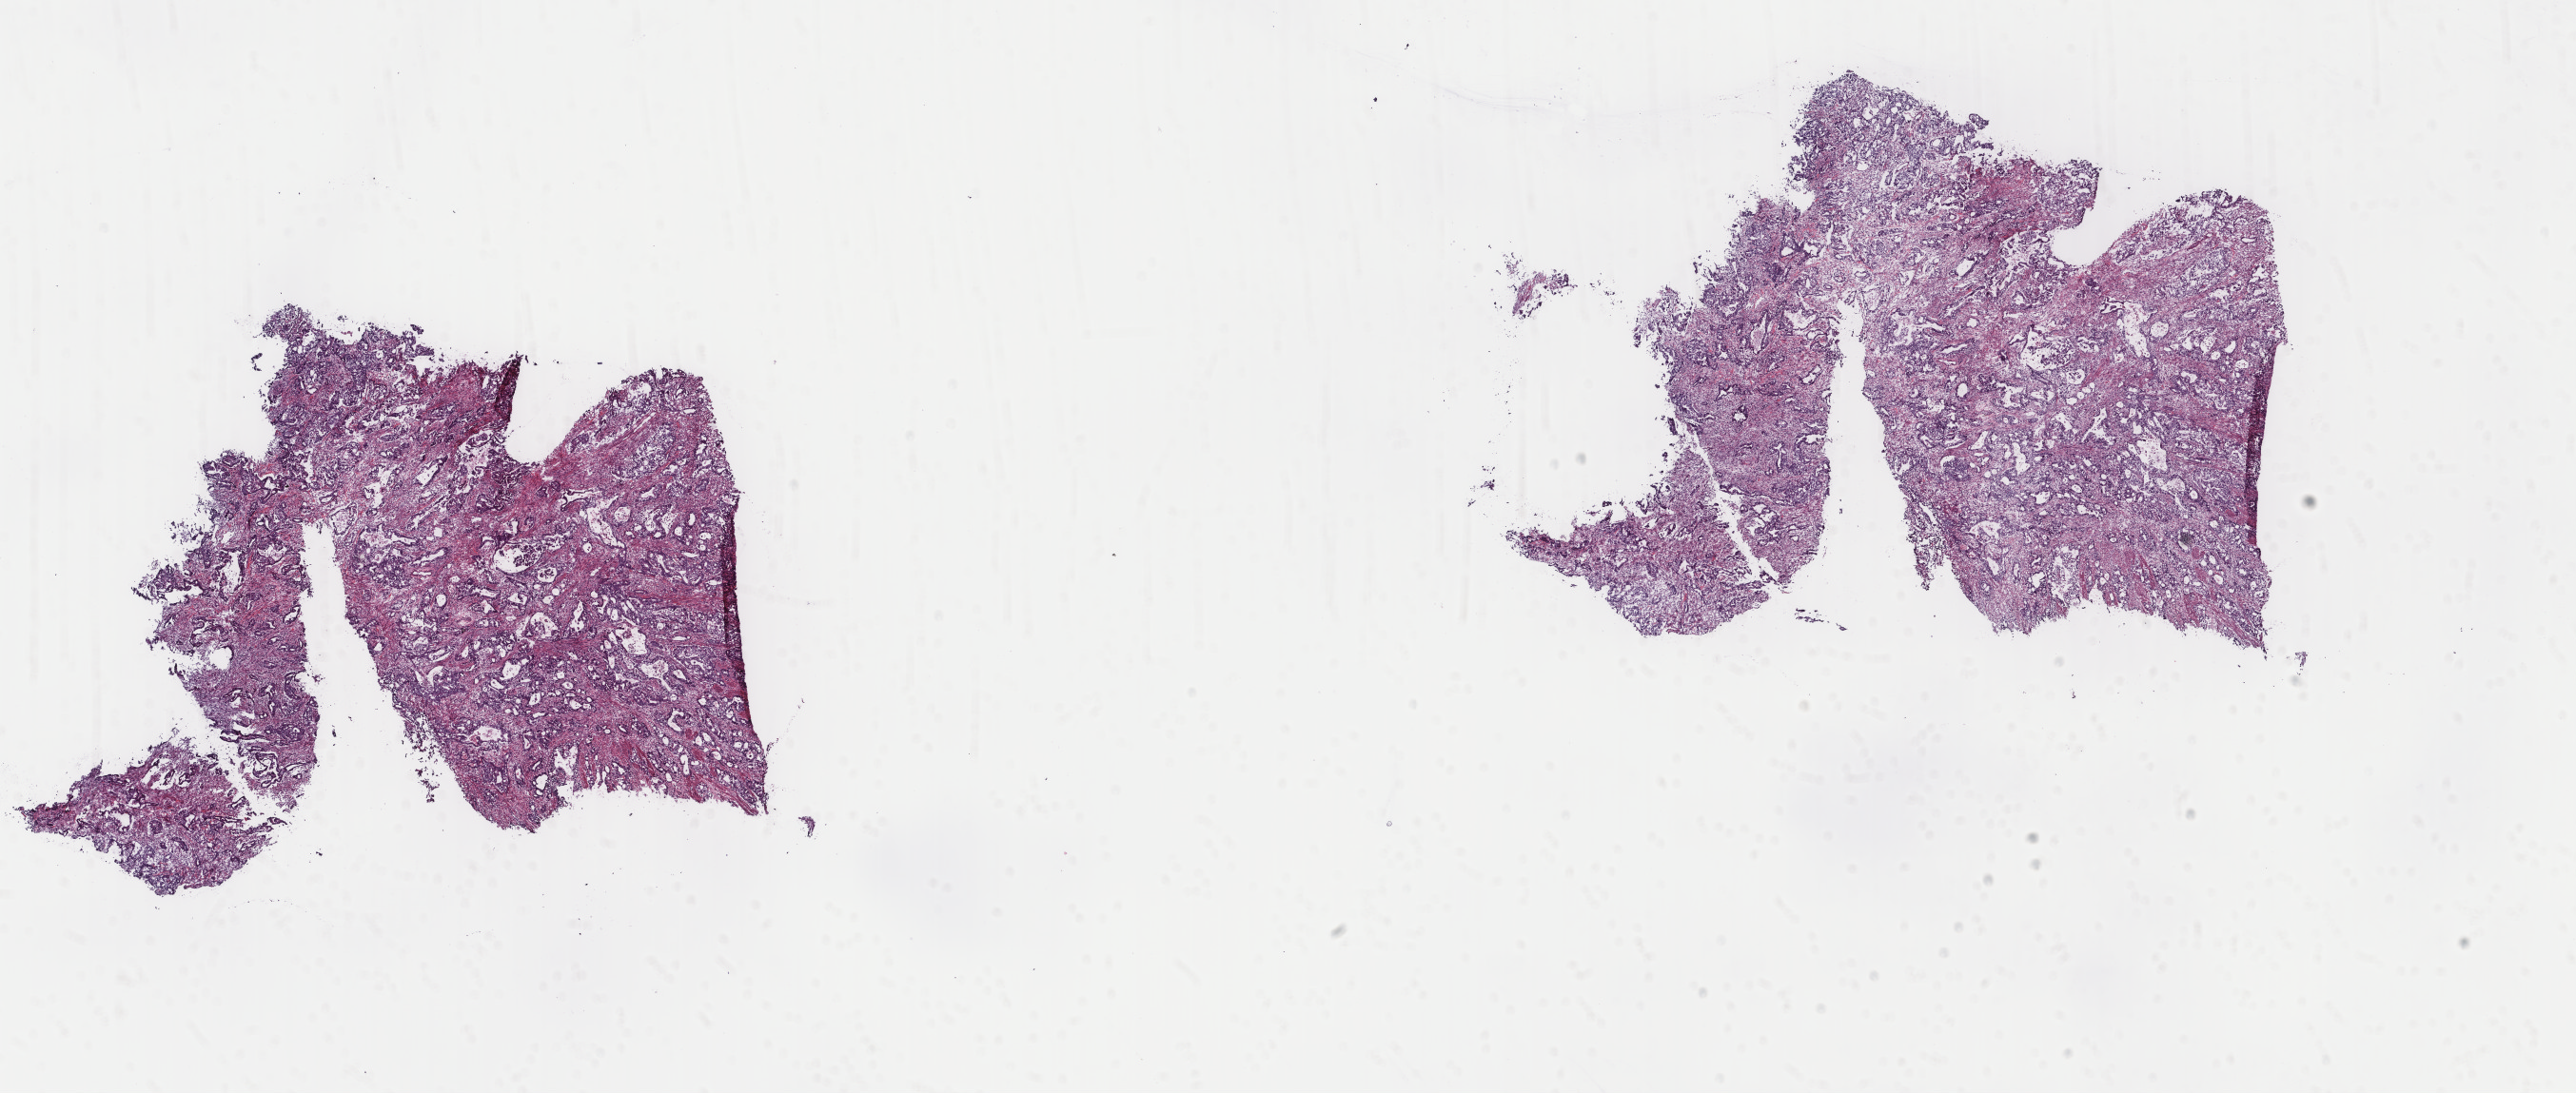
Whole-slide histology image, H&E-stained, whole scanned area (about 21.5 x 9.1 mm, acquisition: 40x scan) shown as a low-resolution overview, frozen section, stomach, primary tumour sample. Male, age 60 years at initial diagnosis. Histologic grade: G2 (moderately differentiated). Composition of this section per pathologist review: tumour cells 50%, tumour nuclei 78%, normal cells 0%, stromal cells 45%, necrosis 5%. Inflammatory infiltration, as recorded: lymphocyte infiltration 10%, monocyte infiltration 2%, neutrophil infiltration 0%.
Histologic diagnosis: Adenocarcinoma, intestinal type (fundus of stomach). AJCC pathologic stage: IIB (7th edition).